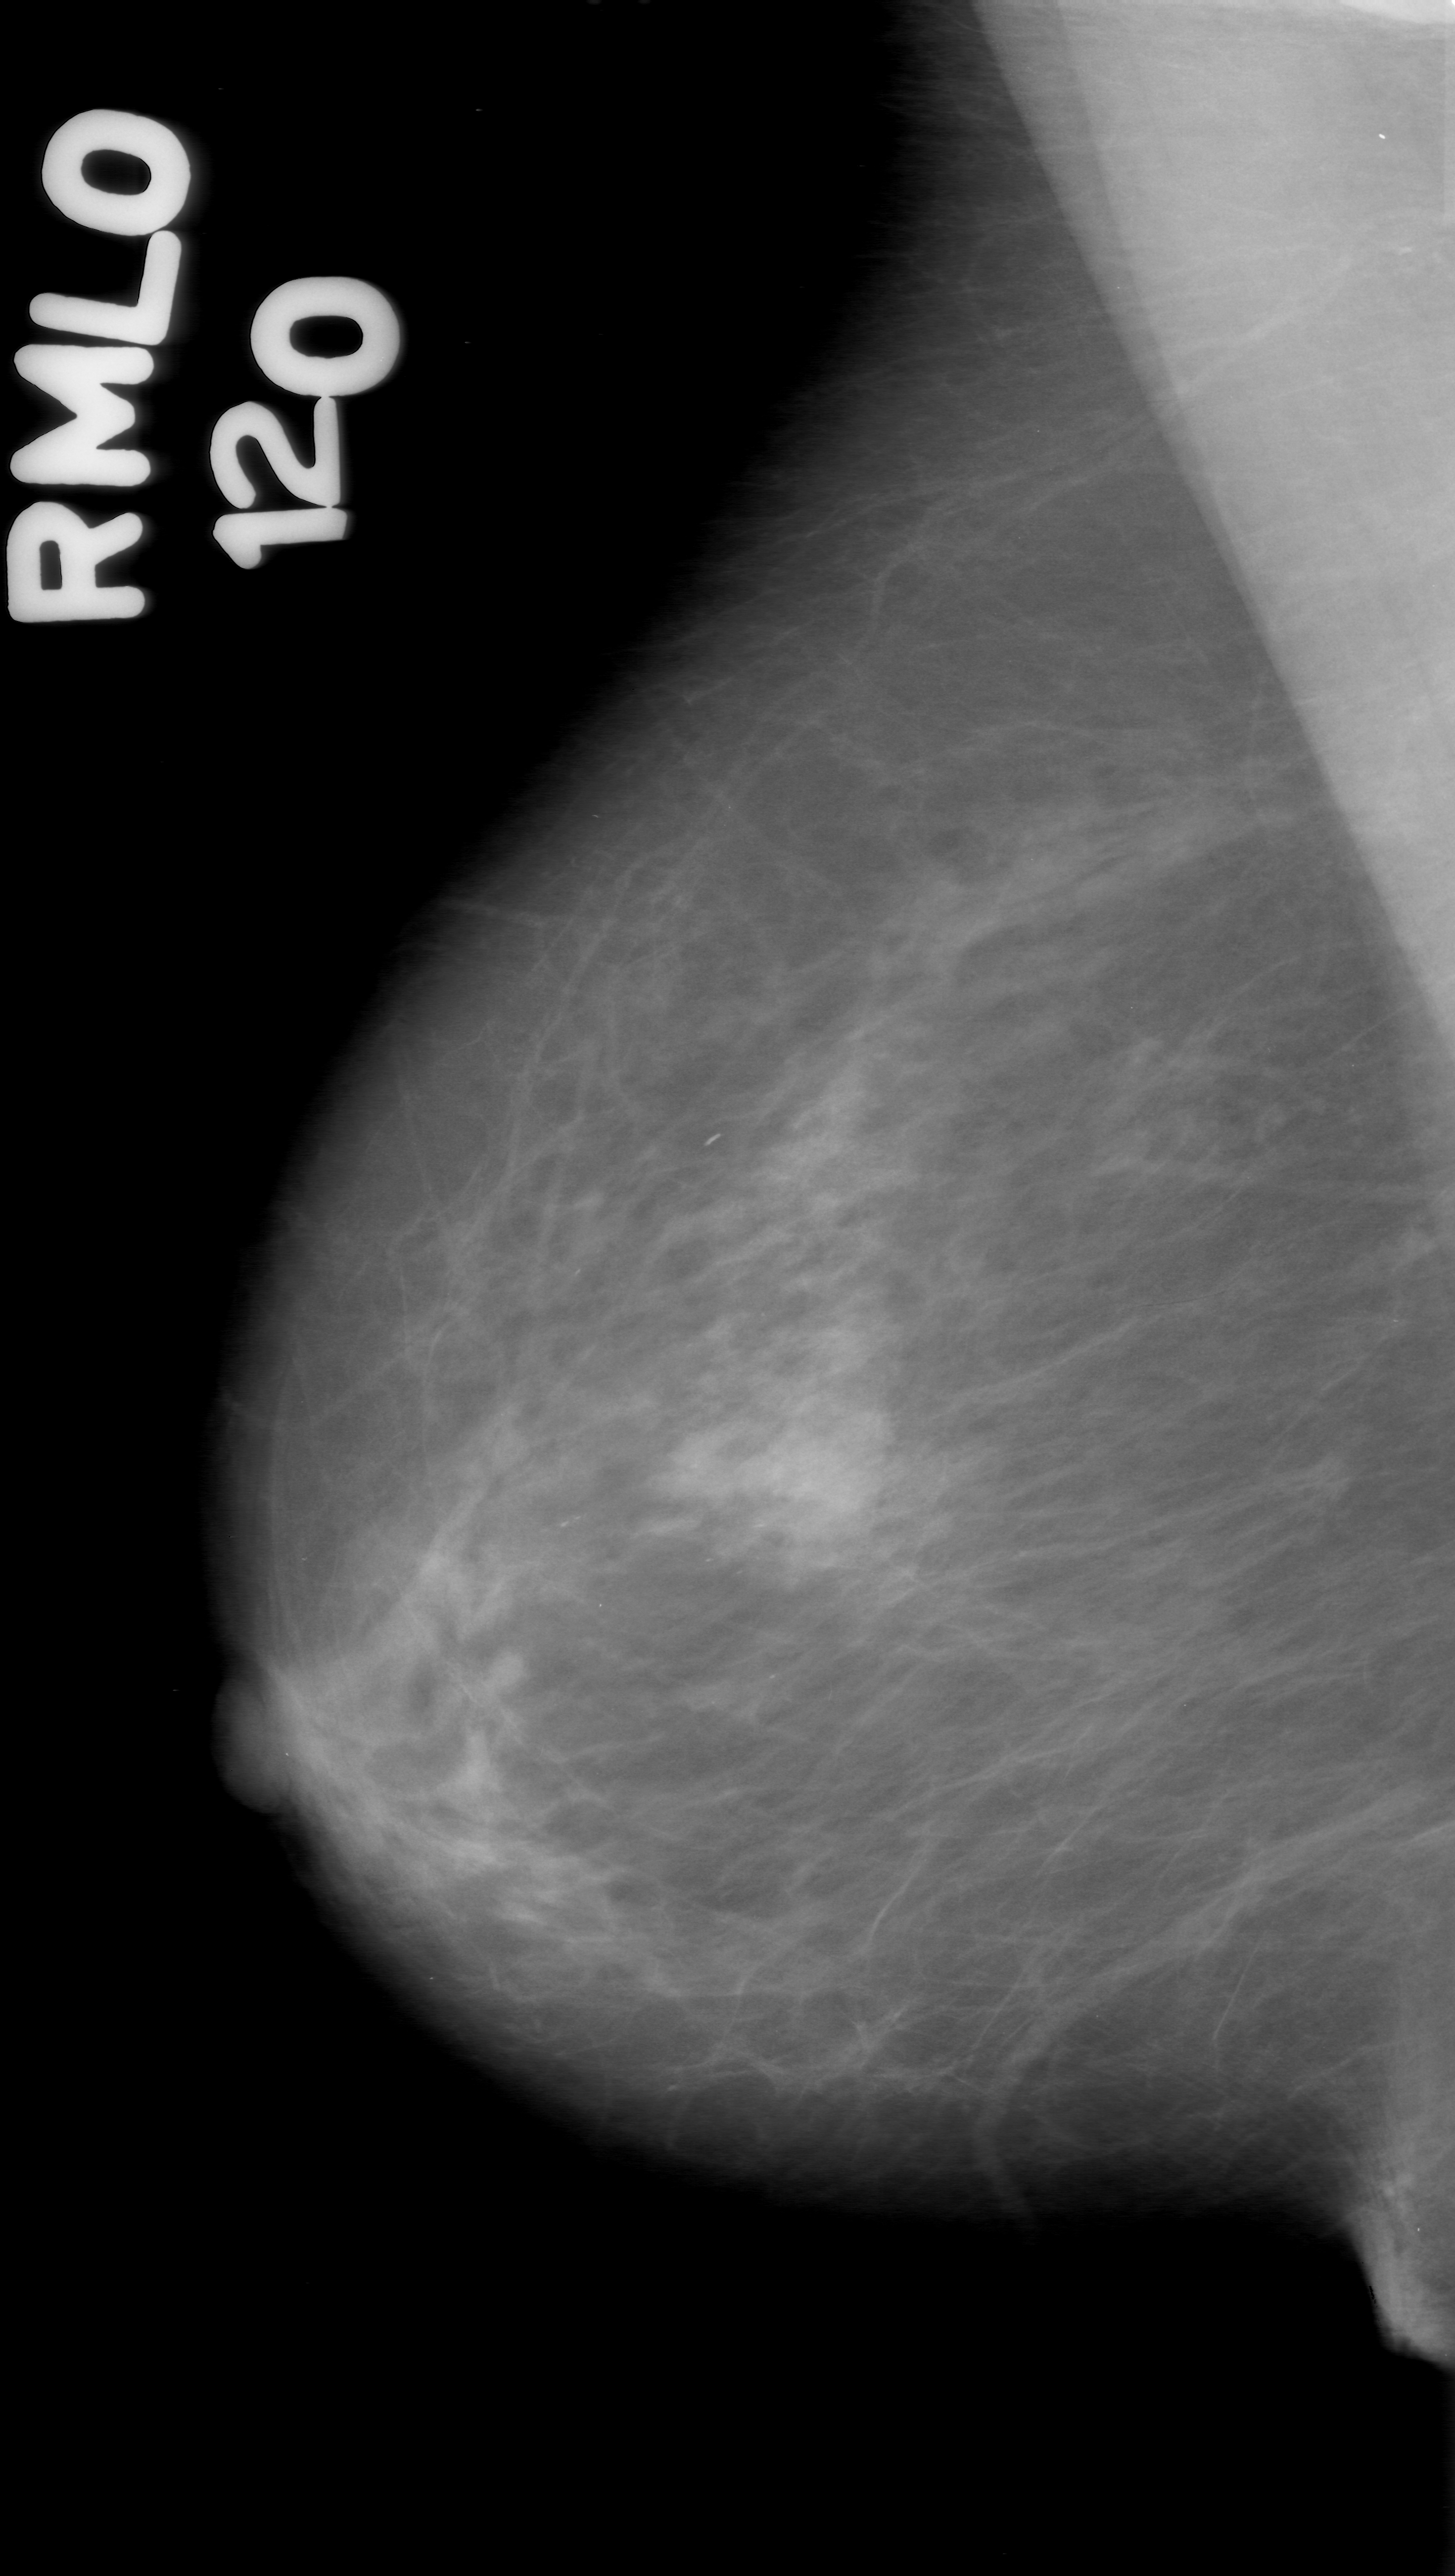
Digitized screen-film mammogram; right breast; mediolateral oblique (MLO) view.
- Mass, shape lobulated, margins obscured; BI-RADS assessment category 0 (incomplete: needs additional imaging); pathology (as recorded): benign.